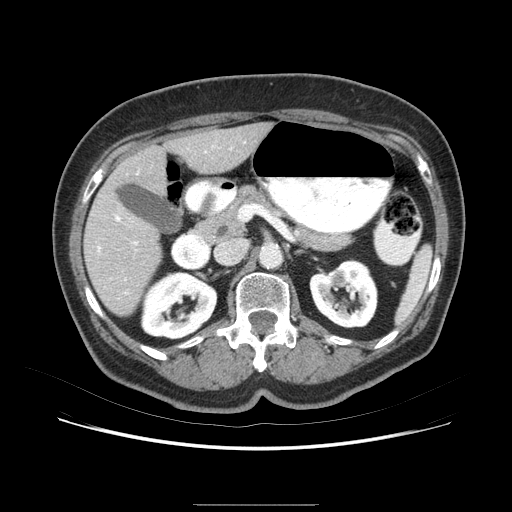
Contrast-enhanced abdominal CT (liver protocol), one axial slice. Slice 35 of 79 in the series (ordered by position). 120 kVp. Soft-tissue window (W 400 / L 40 HU). 2.5 mm slice thickness. 512 × 512 image matrix. Case-level facts recorded for this patient, not image findings: diagnosis: hepatocellular carcinoma (patient treated with transarterial chemoembolisation; whether this scan precedes or follows treatment is not stated here); TNM stage (as recorded): Stage-I; Child-Pugh class: A; tumour differentiation: poorly differentiated; tumour nodularity: uninodular.
Structures marked on this image (semi-automatic segmentation, software-assisted and operator-edited):
- liver parenchyma outside the tumour (the mass and vessels are separate outlines, so this box may not span the whole liver): bounding box <82,122,278,327> (left, top, right, bottom; pixels)
- mass: <115,202,154,230>
- liver vessels: <100,152,237,282>